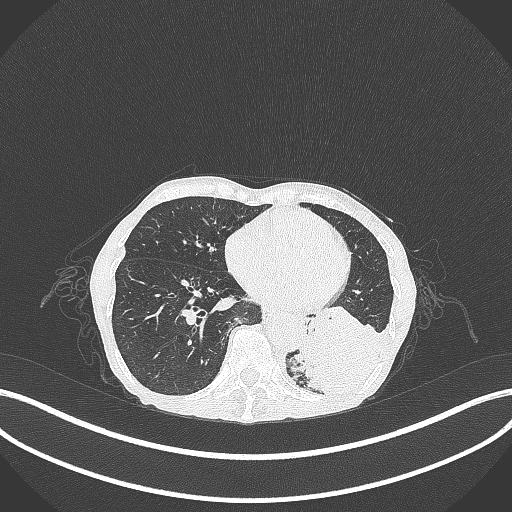
Chest CT, one axial slice; slice 88 of 347 in the series (ordered by position); reconstruction kernel B70f; 120 kVp; lung window (W 1500 / L -600 HU); 1 mm slice thickness; 512 × 512 image matrix. Female patient, age 70 years. From the clinical record (not read from this slice): clinical TNM (as recorded): T3 N0 M0.
Structures marked on this image (bounding box drawn by a radiologist):
- lung tumour (recorded histology: small cell carcinoma): bounding box <296,317,399,400> (left, top, right, bottom; pixels)